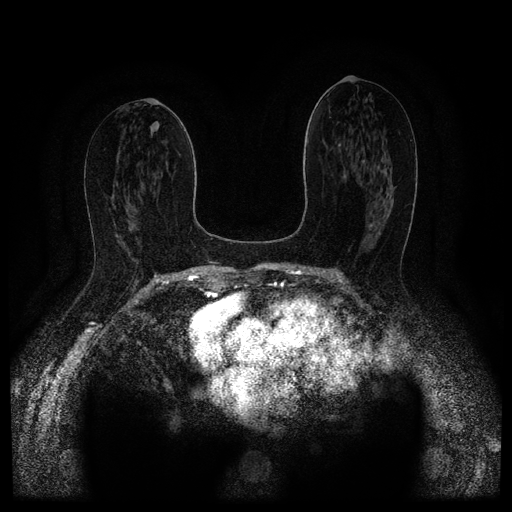
Breast MRI (dynamic contrast-enhanced, multi-phase), one axial slice. Position 55 of 116 along the scan axis. Dynamic contrast-enhanced series, time point 2 of 5 at this slice position (early post-contrast). 1.5 T. TE 2.6 ms, TR 5.4 ms. 512 × 512 image matrix, field of view 340 × 340 mm. Patient: female, 67 years.
Structures marked on this image (semi-automatically segmented with operator editing):
- breast lesion (labelled 'tumour' in the annotation; benign lesions carry a separate 'benign' label): box from (x=369, y=220) to (x=381, y=234) px